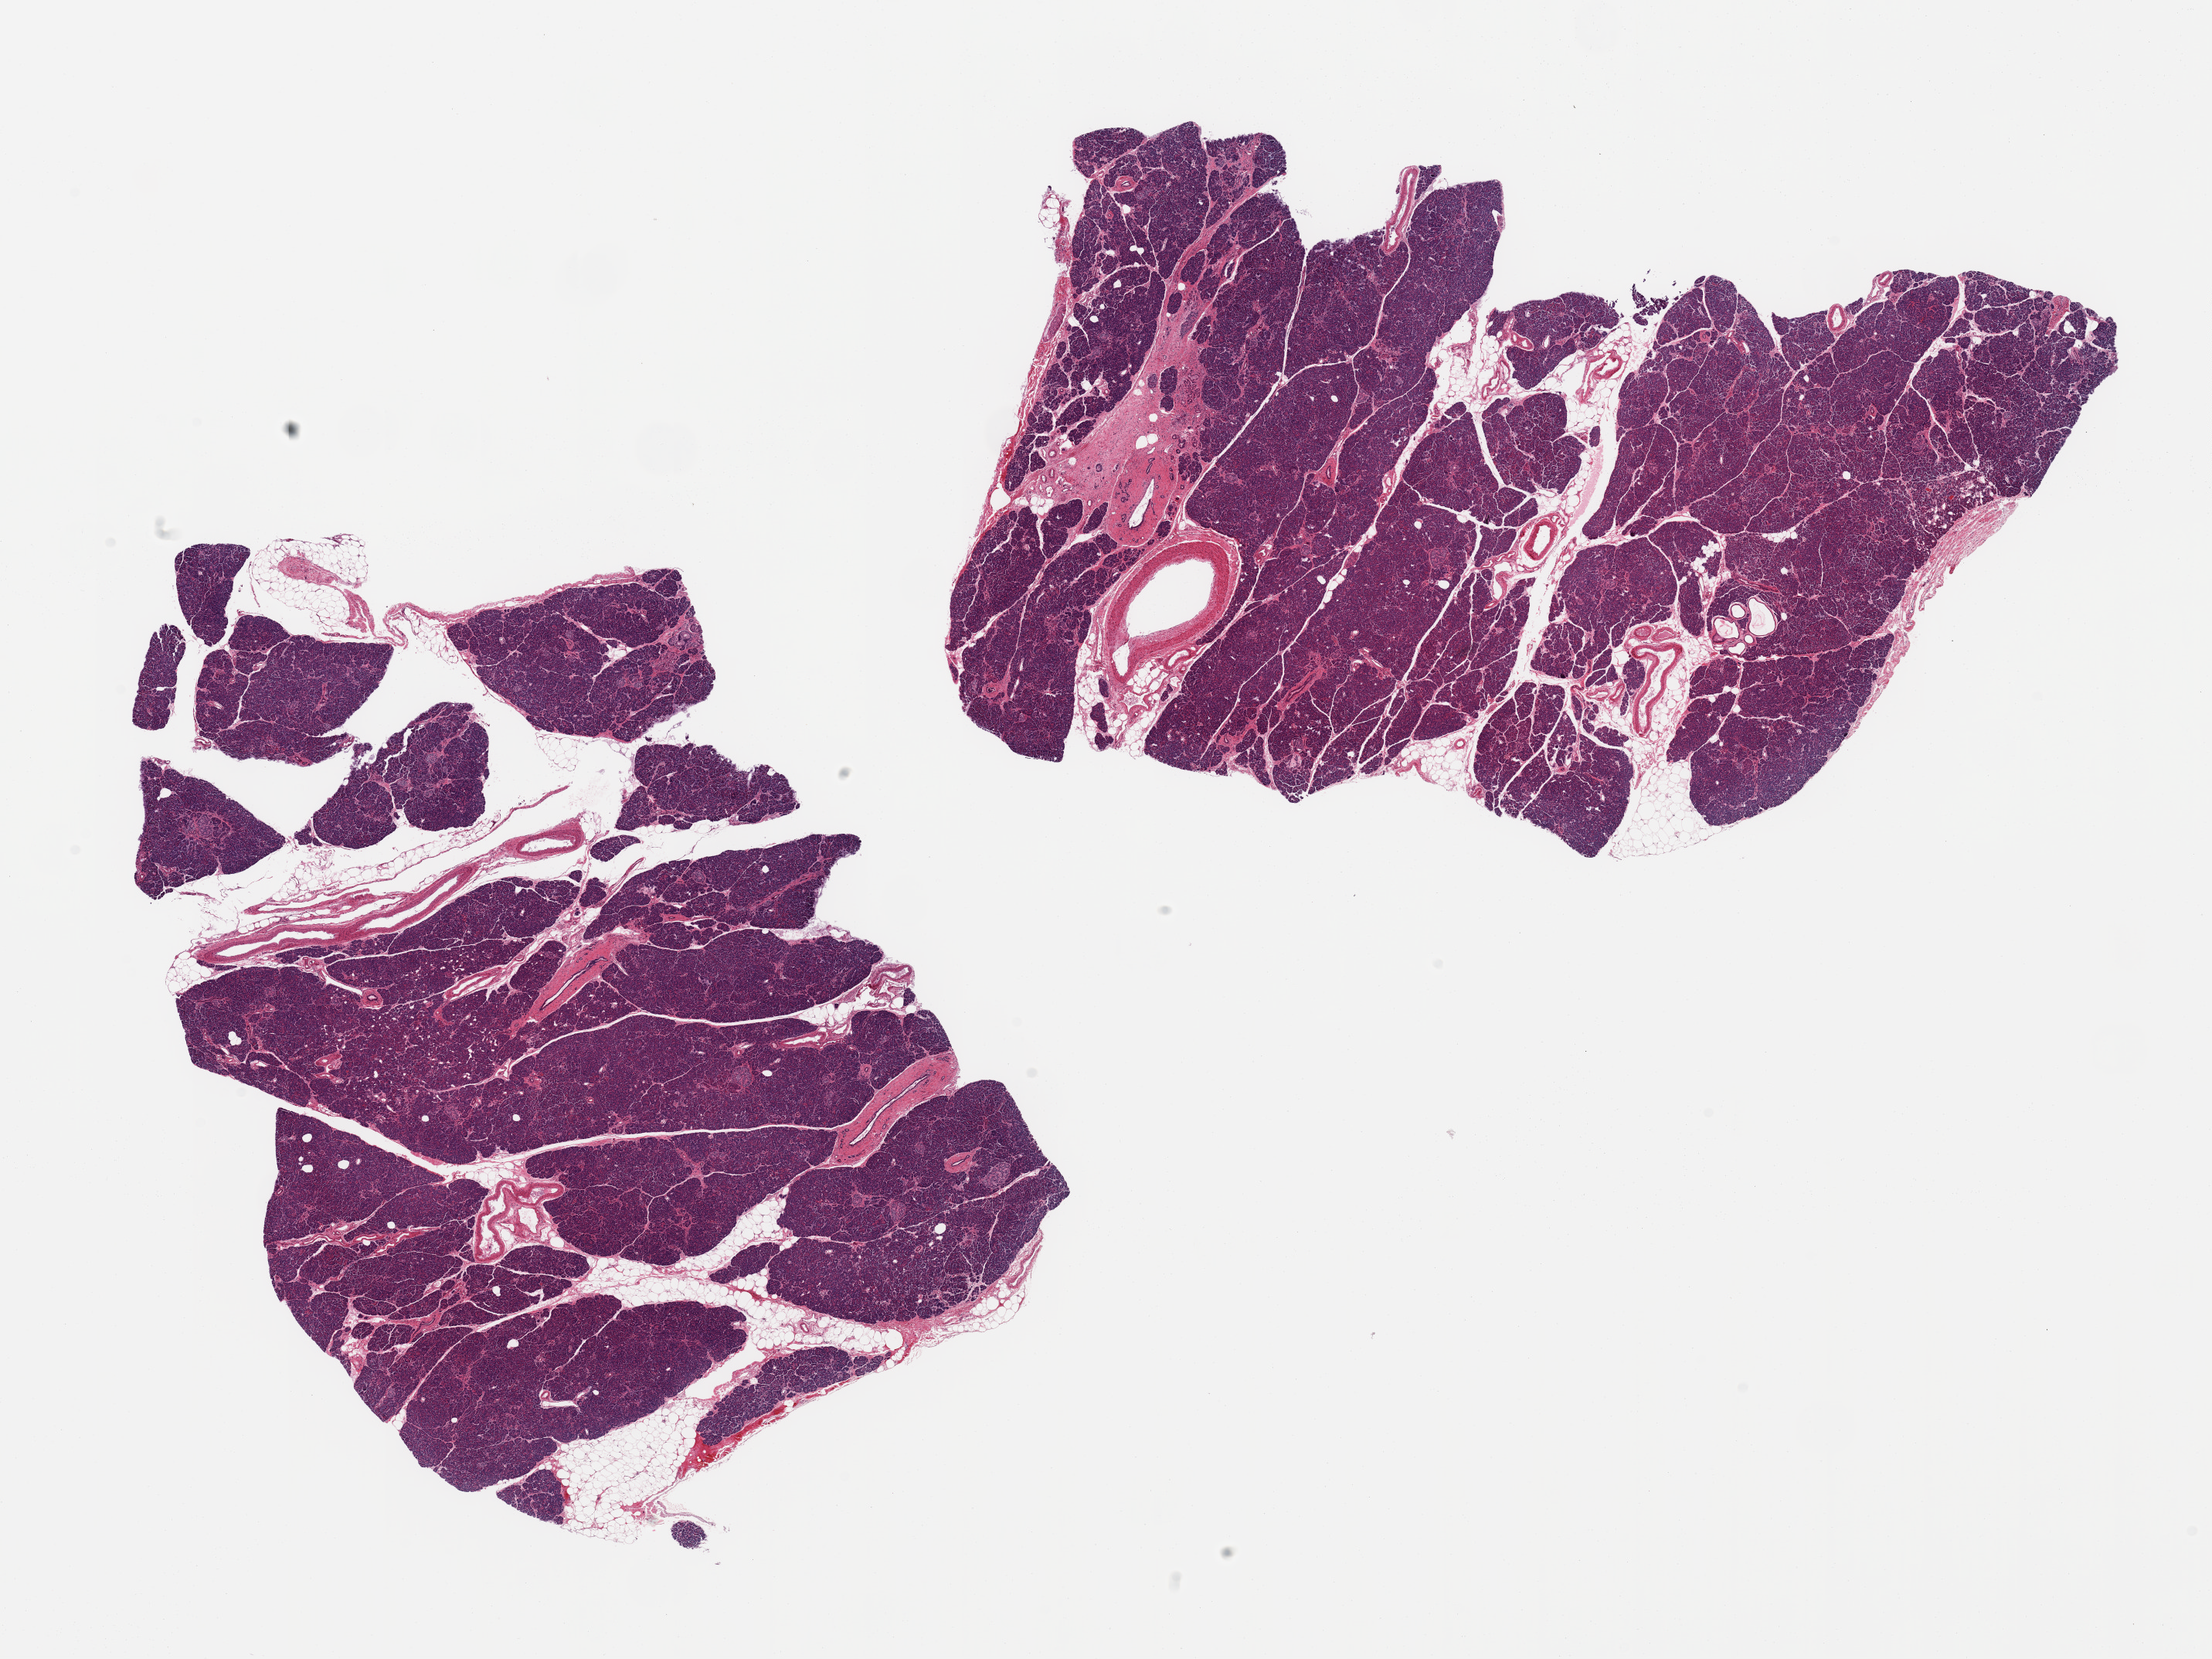
Whole-slide image, hematoxylin and eosin (H&E) stain, brightfield, whole scanned area (about 22.6 x 17.0 mm, slide scanned at 20x) shown as a low-resolution overview. PAXgene-fixed, paraffin-embedded tissue. Sampled site (target tissue): pancreas. Donor tissue sample. Donor: male.
Pathologist's review note for this sample: 2 pieces, Islets well visualized; focal fat.